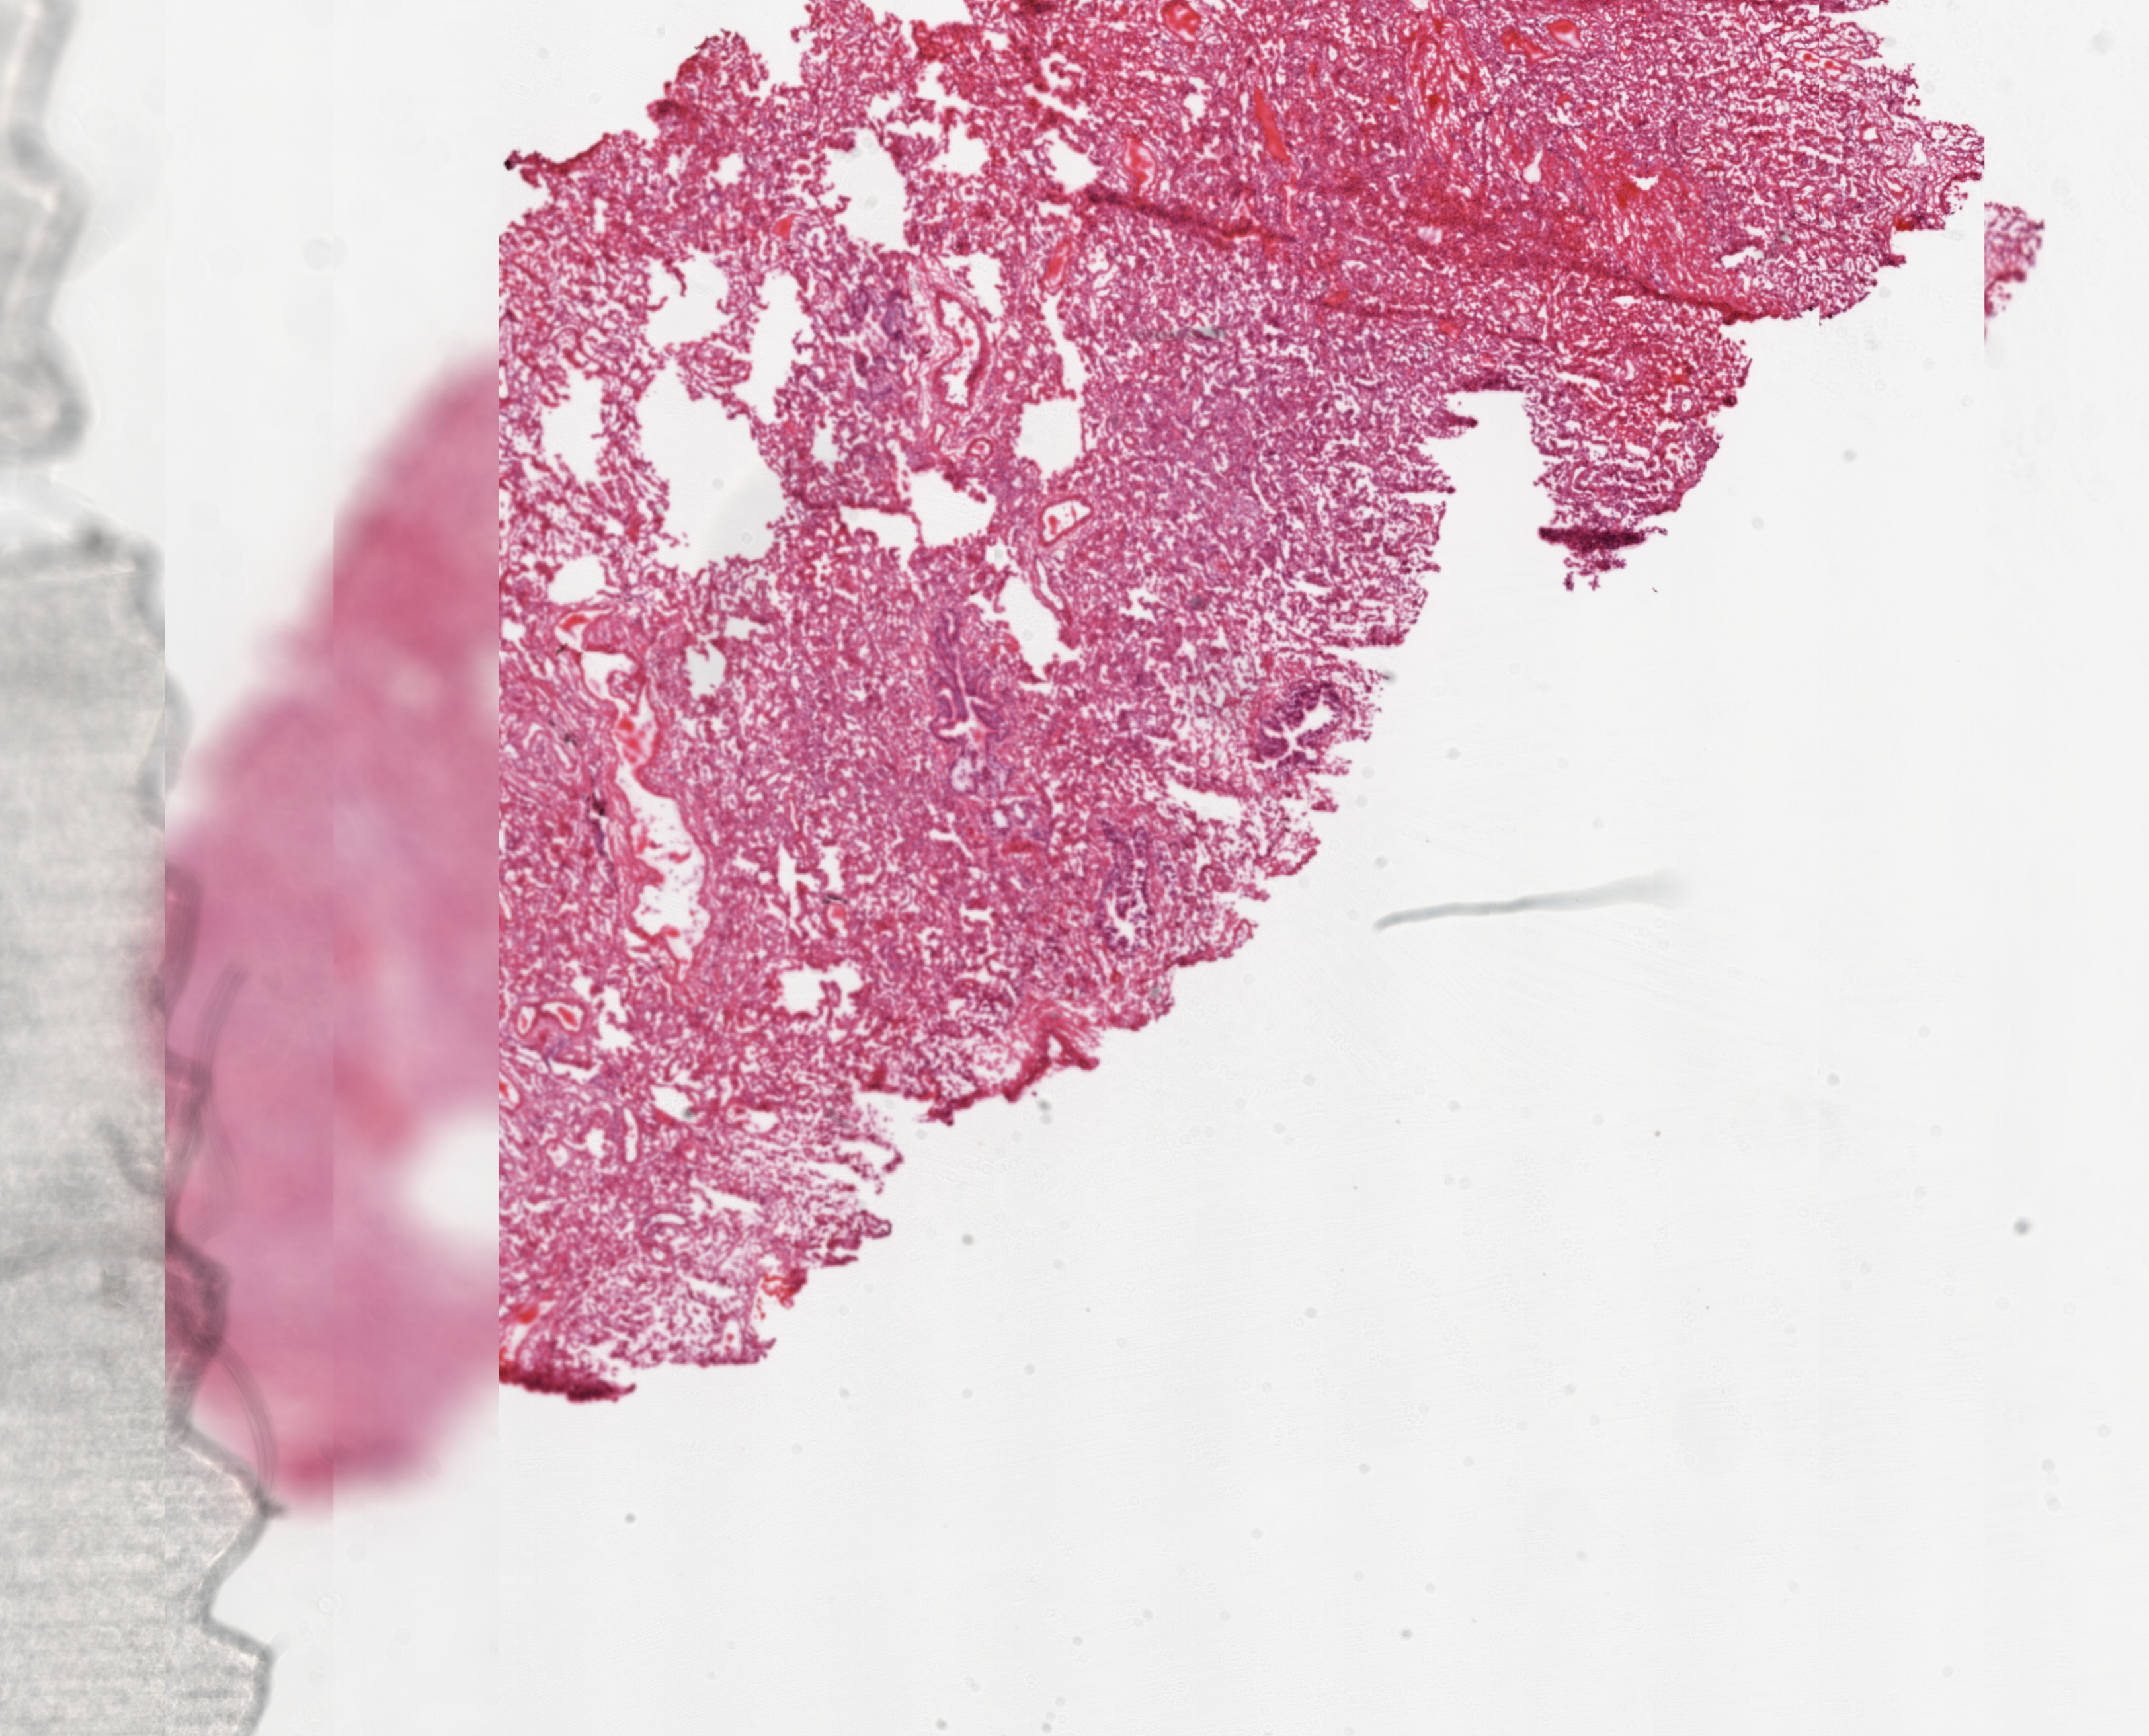
Digitized Hematoxylin and eosin (H&E) stained tissue section (whole slide), shown as a low-resolution overview of the whole scanned area (about 13.0 x 10.5 mm). Frozen section. Sample: solid tissue normal (non-tumour tissue), lung. Male patient; age at initial diagnosis 75 years.
This section: solid tissue normal sample (biorepository sample class). Patient diagnosis: Squamous cell carcinoma, NOS (lower lobe, lung).